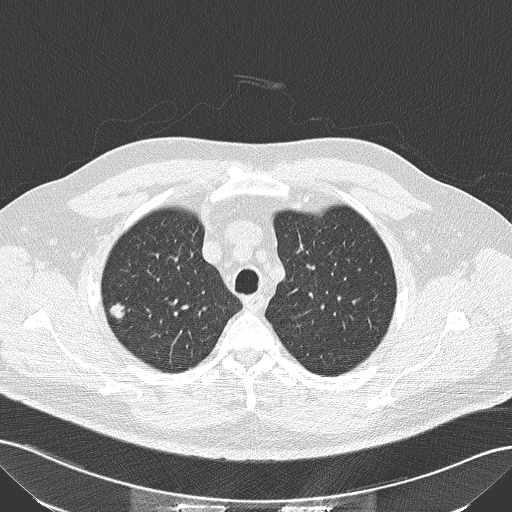
Low-dose screening chest CT, one axial slice. Slice 120 of 152 in the series (ordered by position). 120 kVp. Lung window (W 1500 / L -600 HU). 2 mm slice thickness. 512 × 512 image matrix, field of view 360 × 360 mm.
Structures marked on this image (outlined manually by an expert reader):
- lesion 1 (tumor, upper lobe of right lung): box from (x=110, y=302) to (x=126, y=319) px